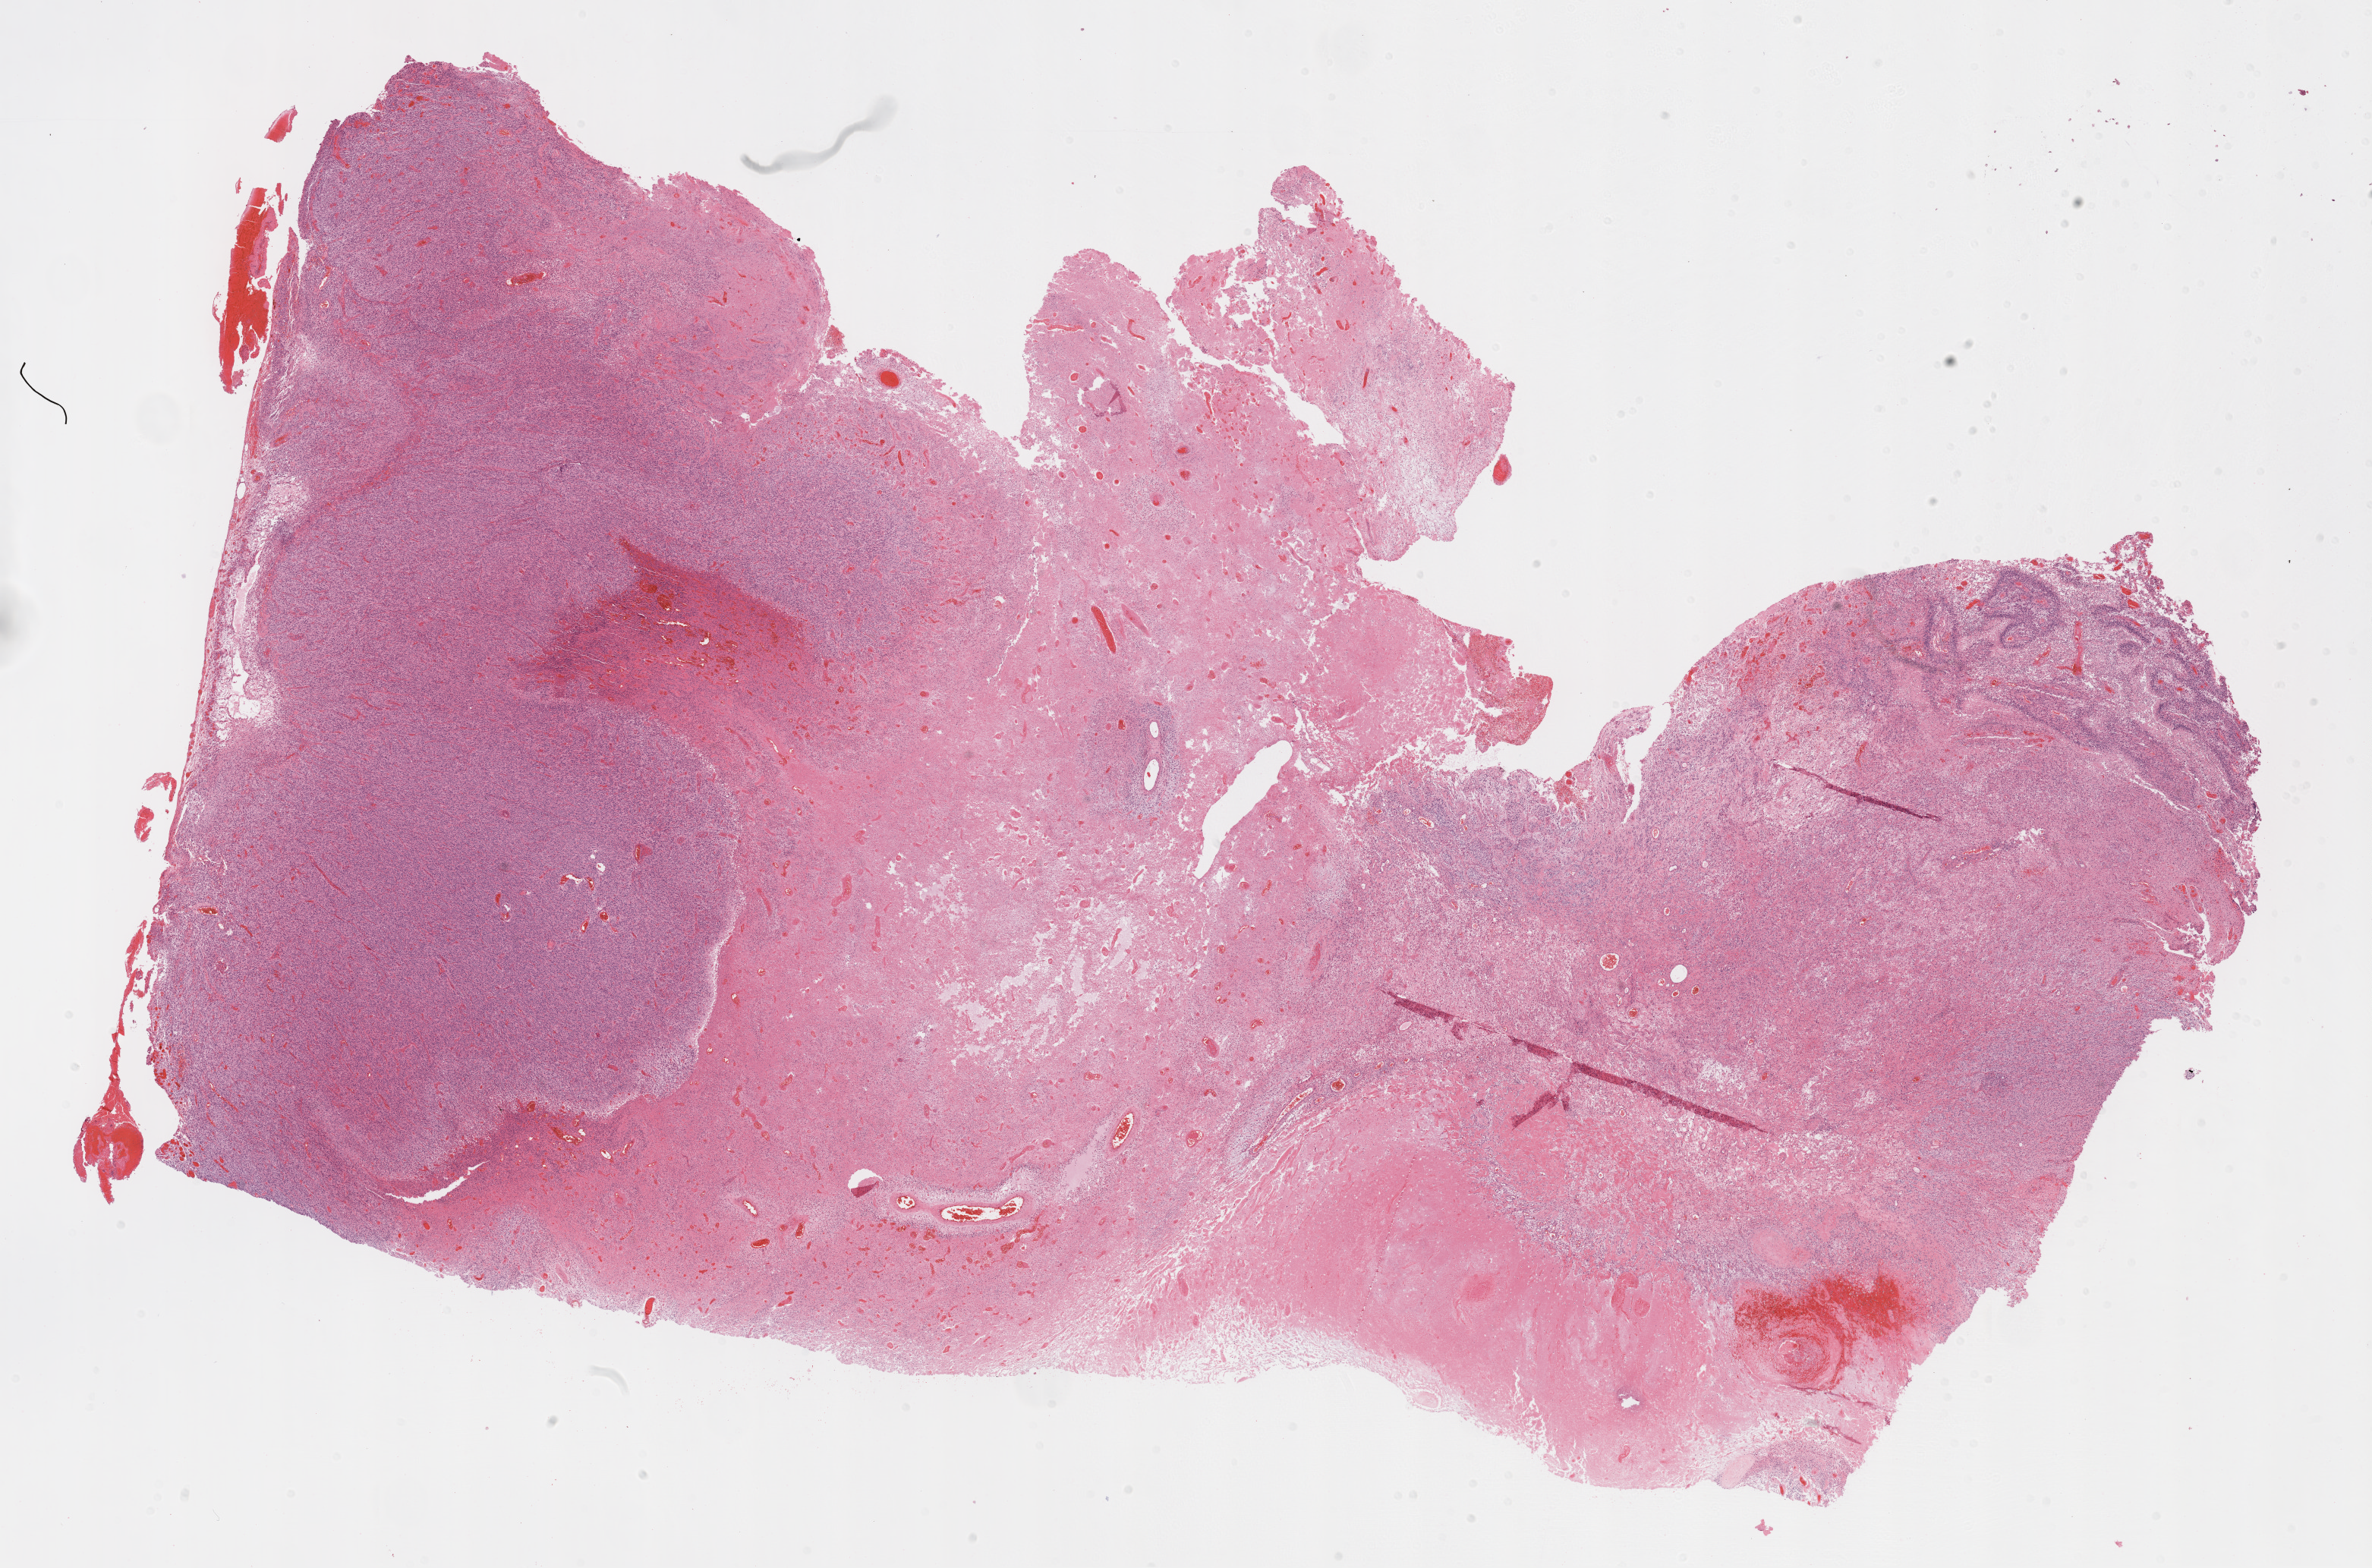
H&E whole-slide image — shown as a low-resolution overview of the whole scanned area (about 25.1 x 16.6 mm, acquisition: 20x scan); FFPE section; primary tumour sample from the brain. Female patient; age at initial diagnosis 63 years.
Pathologic diagnosis: Glioblastoma.